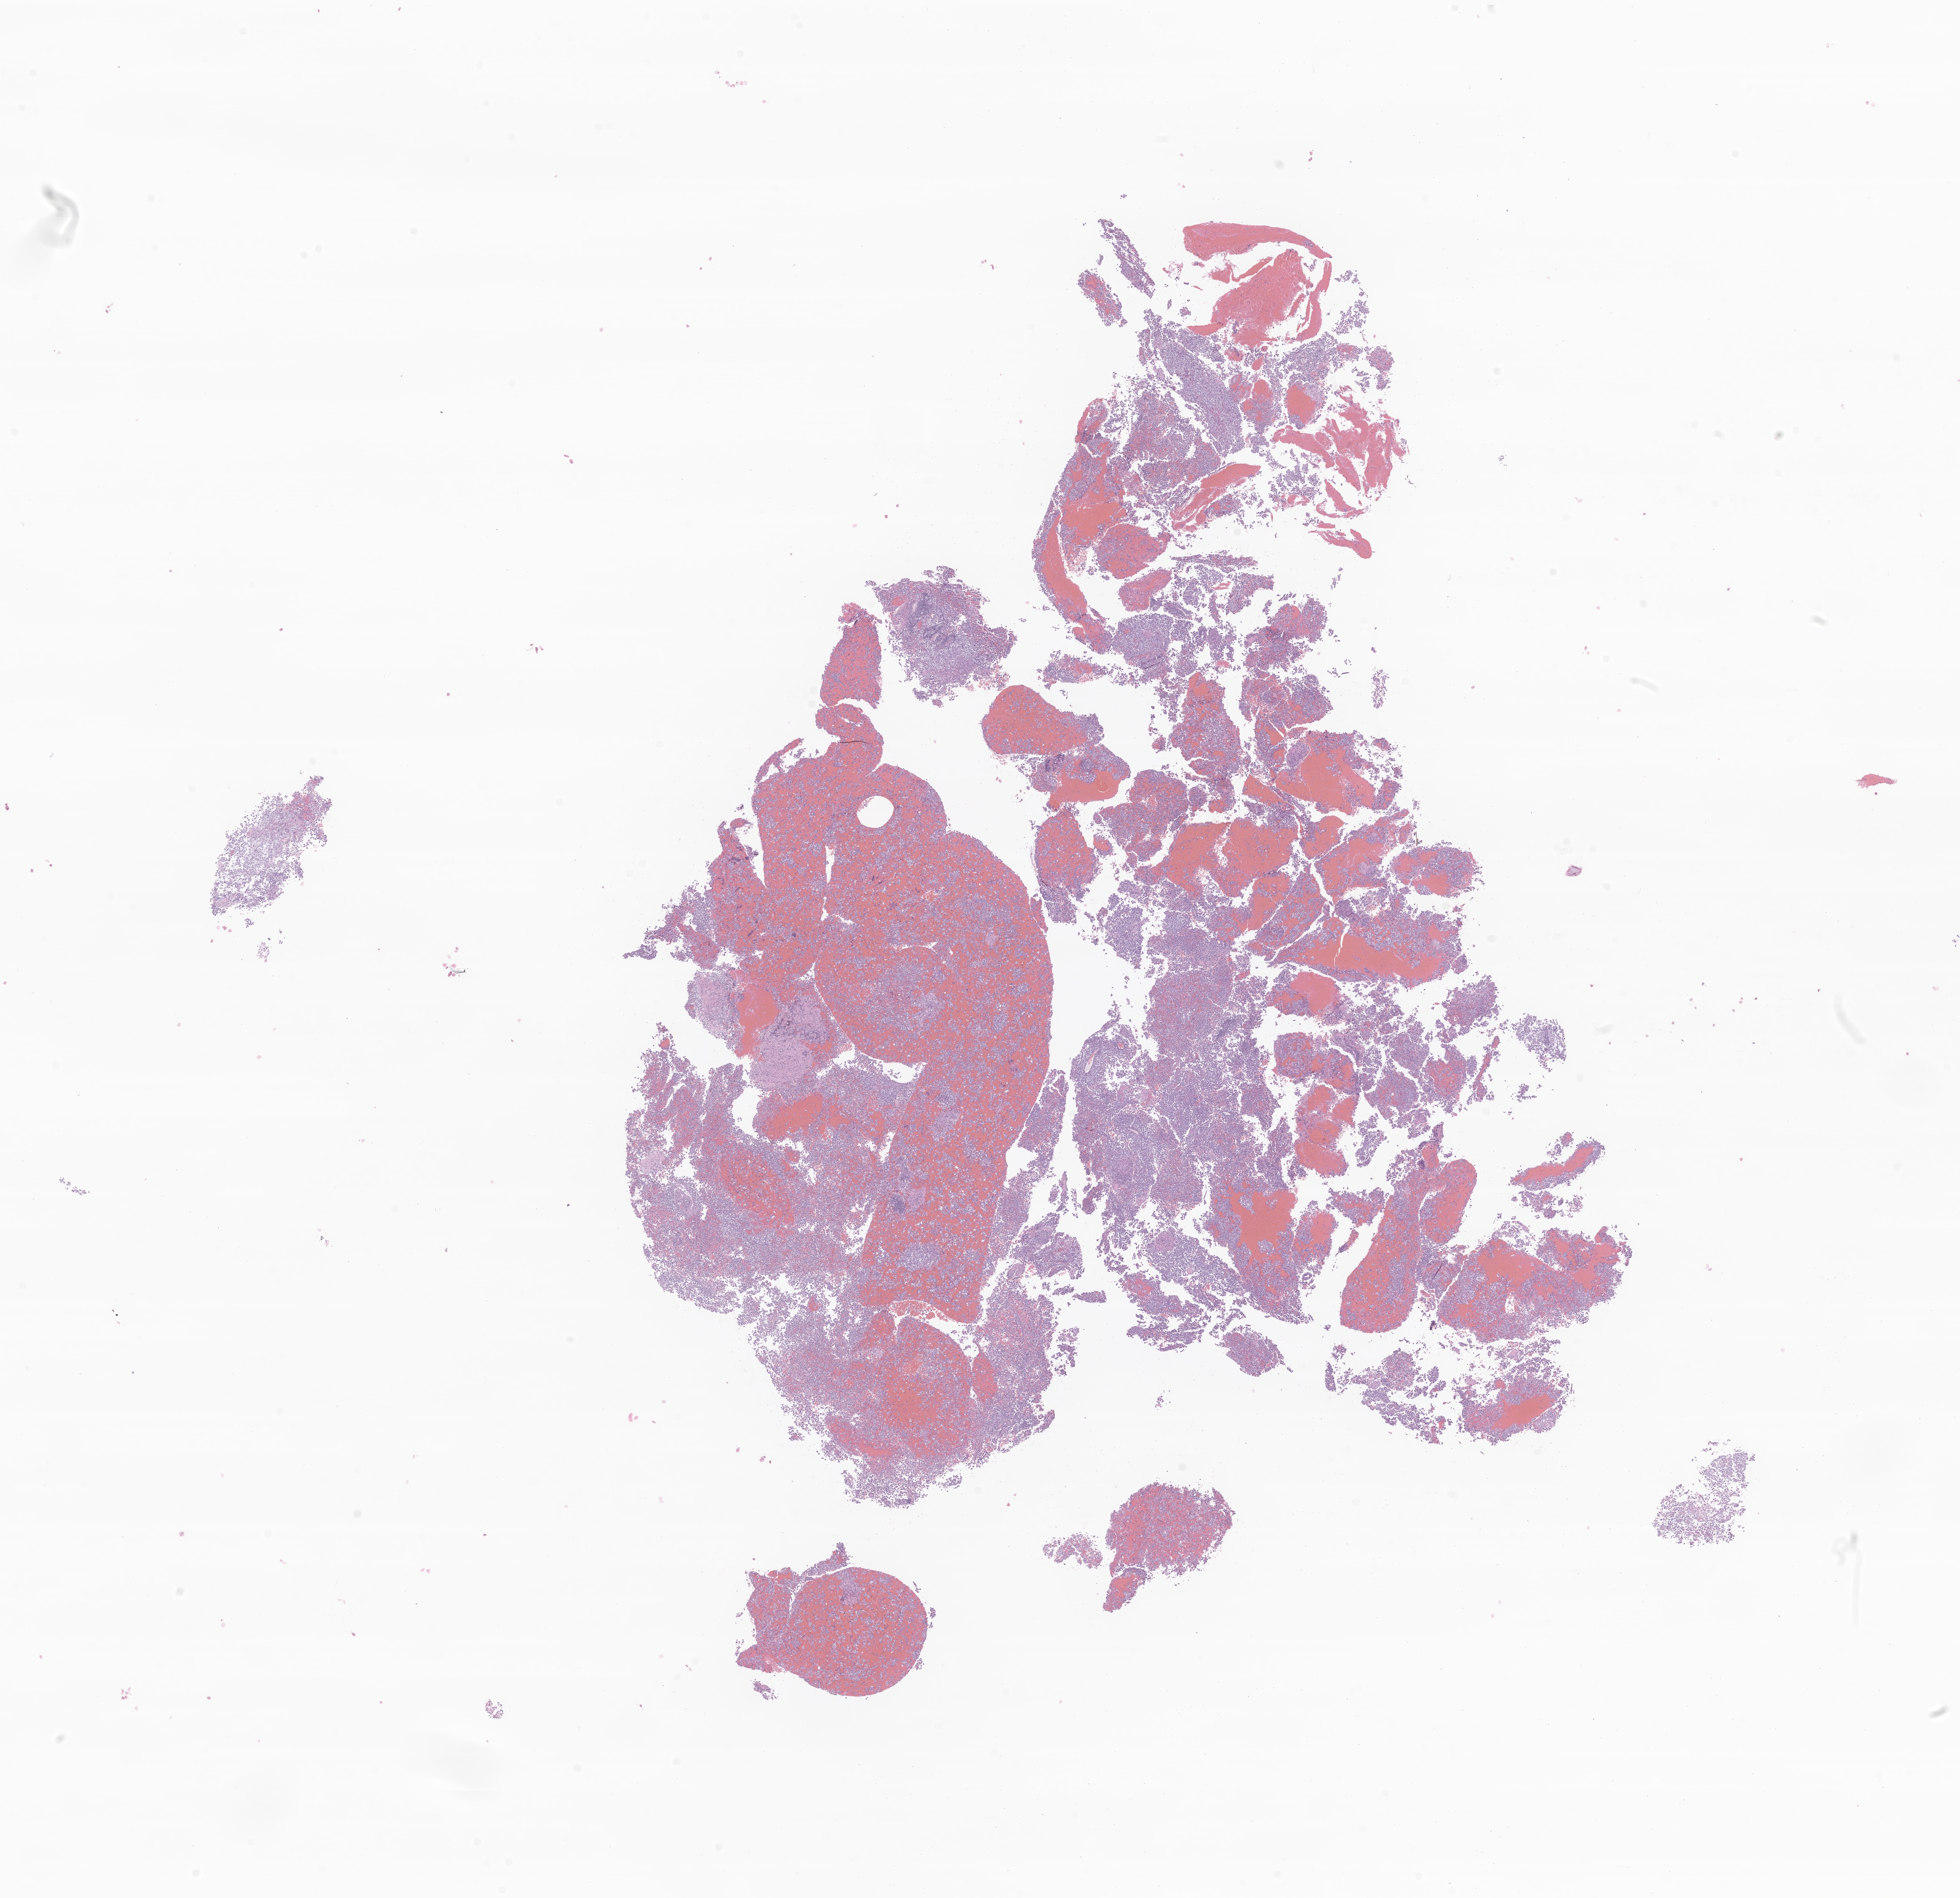
Digitized haematoxylin and eosin-stained section of tumor tissue from the brain, a low-resolution overview of the entire scanned area, about 18.6 x 18.0 mm. FFPE section. Patient female; age 186 months (15 years 6 months).
Diagnosis: Germinoma.